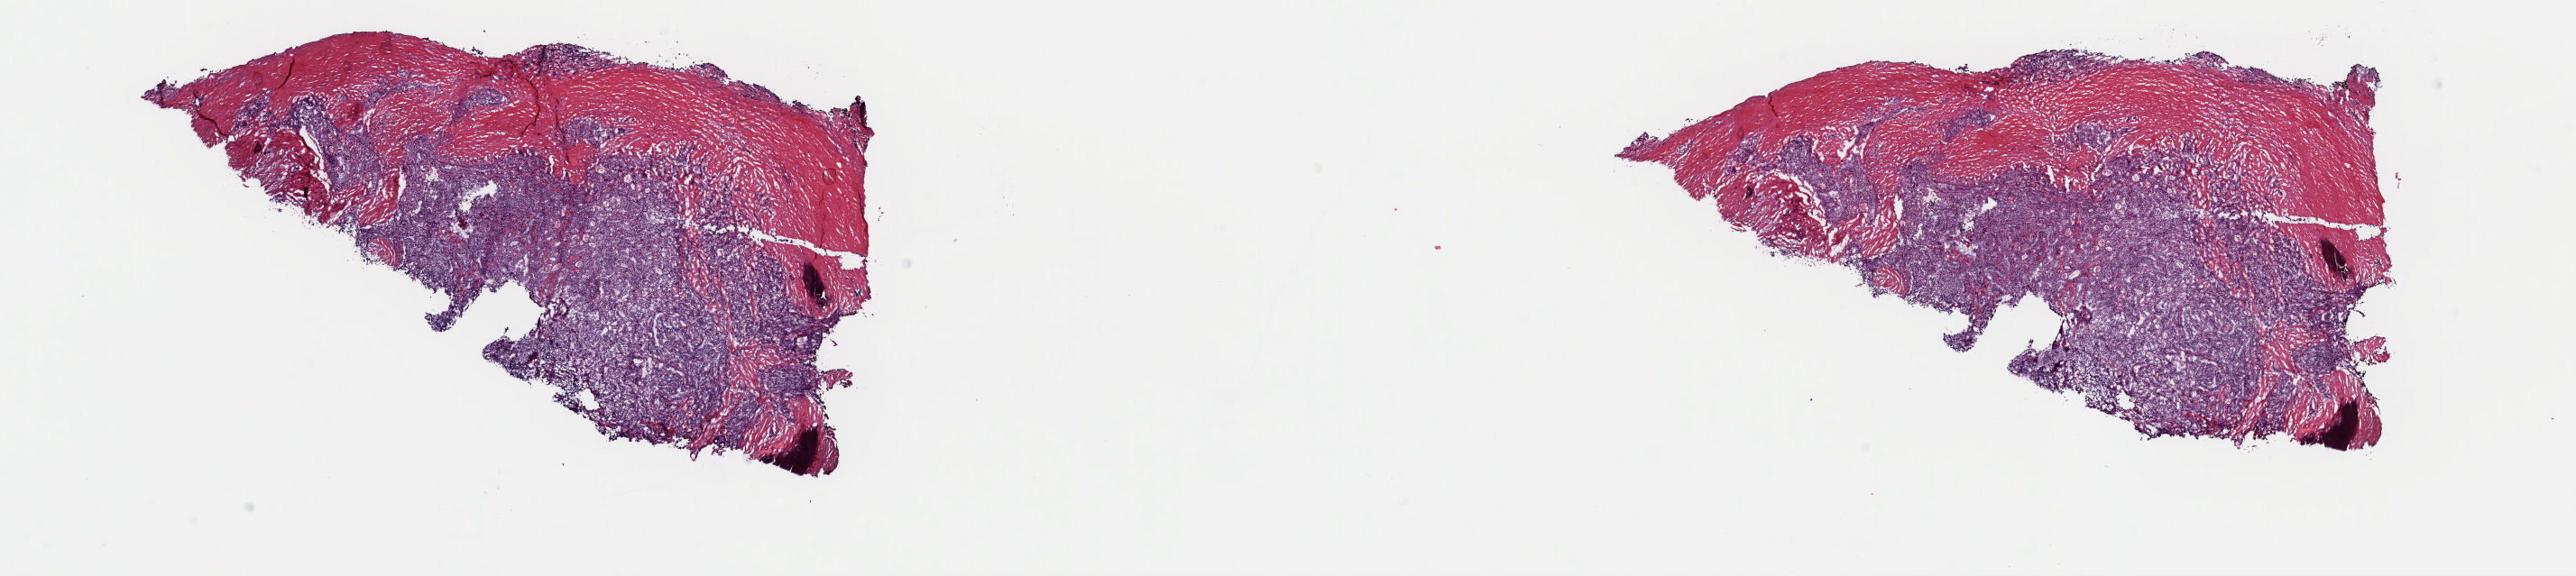
Digitized H&E tissue section (whole slide) — whole scanned area (about 22.6 x 5.0 mm) shown as a low-resolution overview. Frozen section from the top of the tissue portion. Thyroid, primary tumour sample. Female patient; age at initial diagnosis 50 years. Composition of this section per pathologist review: tumour cells 75%, tumour nuclei 75%, normal cells 0%, stromal cells 25%, necrosis 0%. Inflammatory infiltration, as recorded: lymphocyte infiltration 3%, monocyte infiltration 1%, neutrophil infiltration 1%.
* lymph nodes positive (case pathology): 0 of 4 examined
* laterality: left
* AJCC pathologic stage: I (6th edition)
* diagnosis: Papillary adenocarcinoma, NOS (thyroid gland)